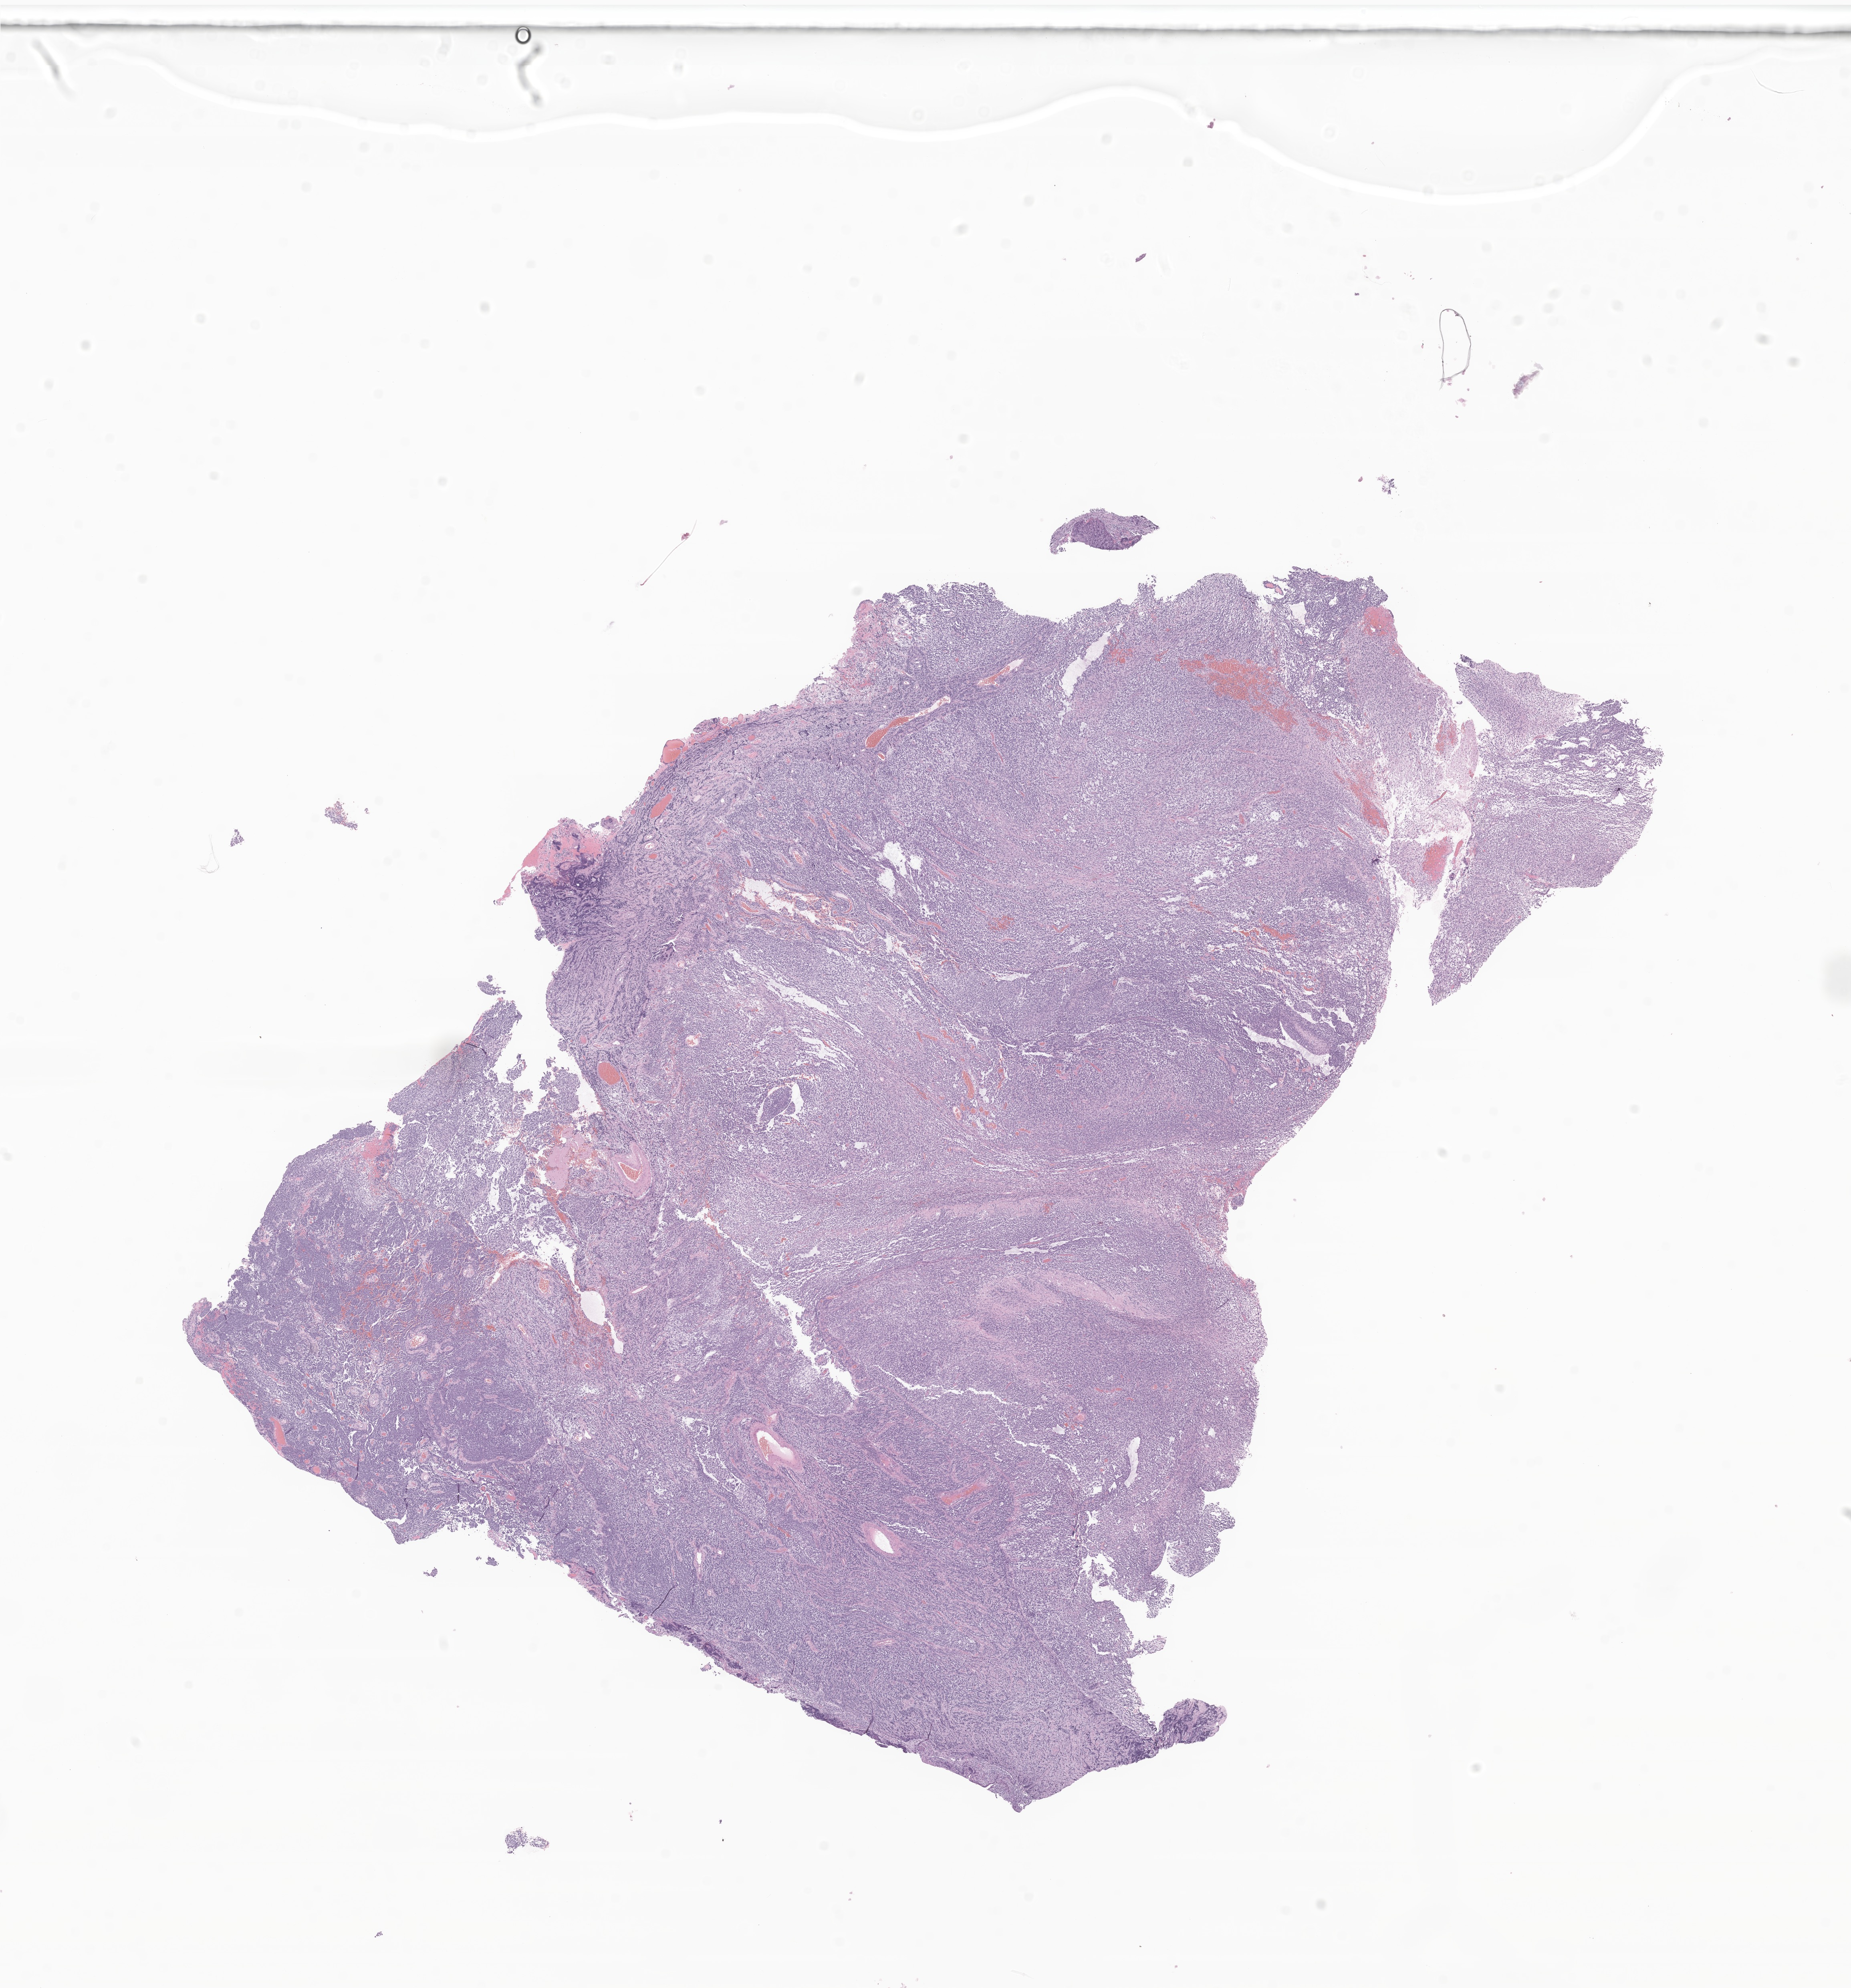
Whole-slide image, H&E stain of tumor tissue from the brain, a low-resolution overview of the entire scanned area, about 19.5 x 20.9 mm, FFPE section. Patient: female, age 146 months.
Recorded diagnosis: Medulloblastoma, NOS.